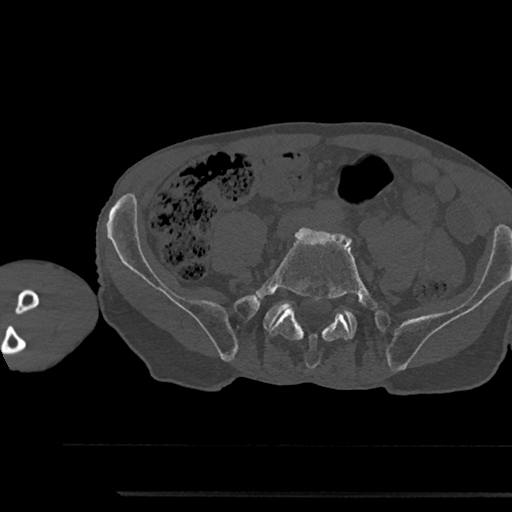
CT including the spine, one axial slice. Slice 339 of 797 in the series (ordered by position). 120 kVp. Bone window (W 1800 / L 400 HU). 512 × 512 image matrix, field of view 367 × 367 mm. Patient: male, 79 years. From the clinical record (not read from this slice): primary cancer: prostate.
Outlined on this slice (semi-automatic segmentation, software-assisted and operator-edited):
- L5 vertebra: bounding box [x1, y1, x2, y2] px = [254, 227, 379, 369]